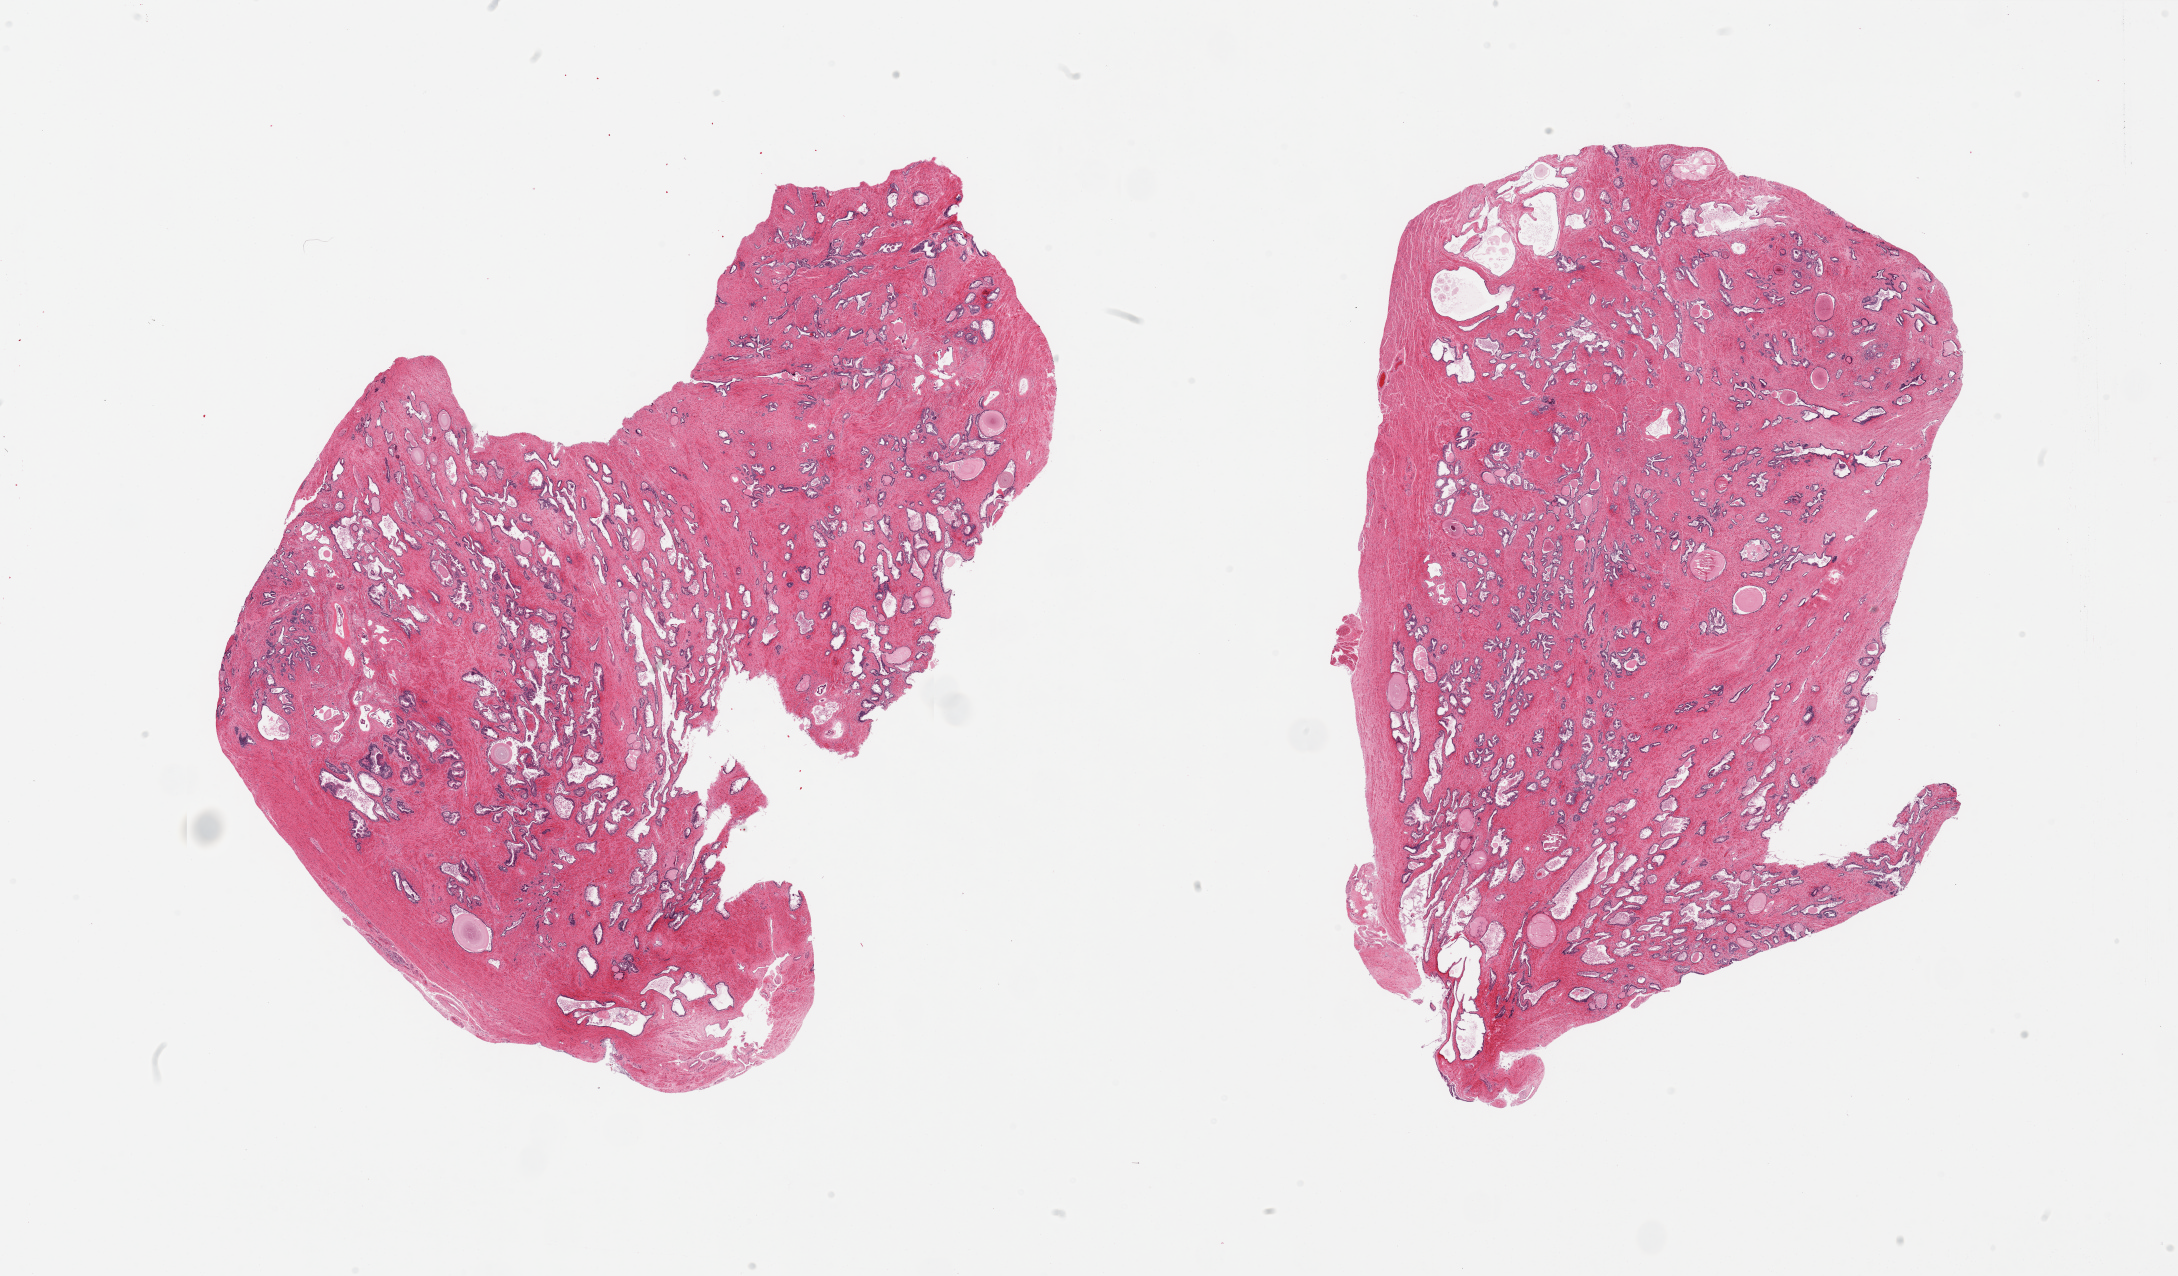
Whole-slide image, H&E stain, low-resolution overview of the scanned area, about 34.5 x 20.2 mm, PAXgene-fixed paraffin-embedded (PFPE) section, target tissue: prostate, tissue donor sample. Male donor.
Reviewer comment on this tissue sample: 2 pieces, glandular epithelium modetately well preserved.